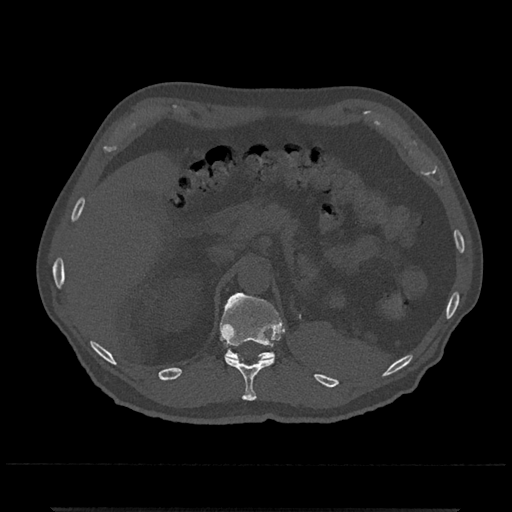
CT including the spine, one axial slice. Position 462 of 797 along the scan axis. Reconstruction kernel Br40s/3. 120 kVp. Bone window (W 1800 / L 400 HU). 512 × 512 image matrix, field of view 393 × 393 mm. Patient: male, 67 years. Case-level facts recorded for this patient, not image findings: primary cancer: prostate.
Annotated regions visible in this slice (semi-automatic segmentation, software-assisted and operator-edited):
- T11 vertebra: box from (x=225, y=356) to (x=275, y=401) px
- T12 vertebra: (x=220, y=293)–(x=285, y=361)